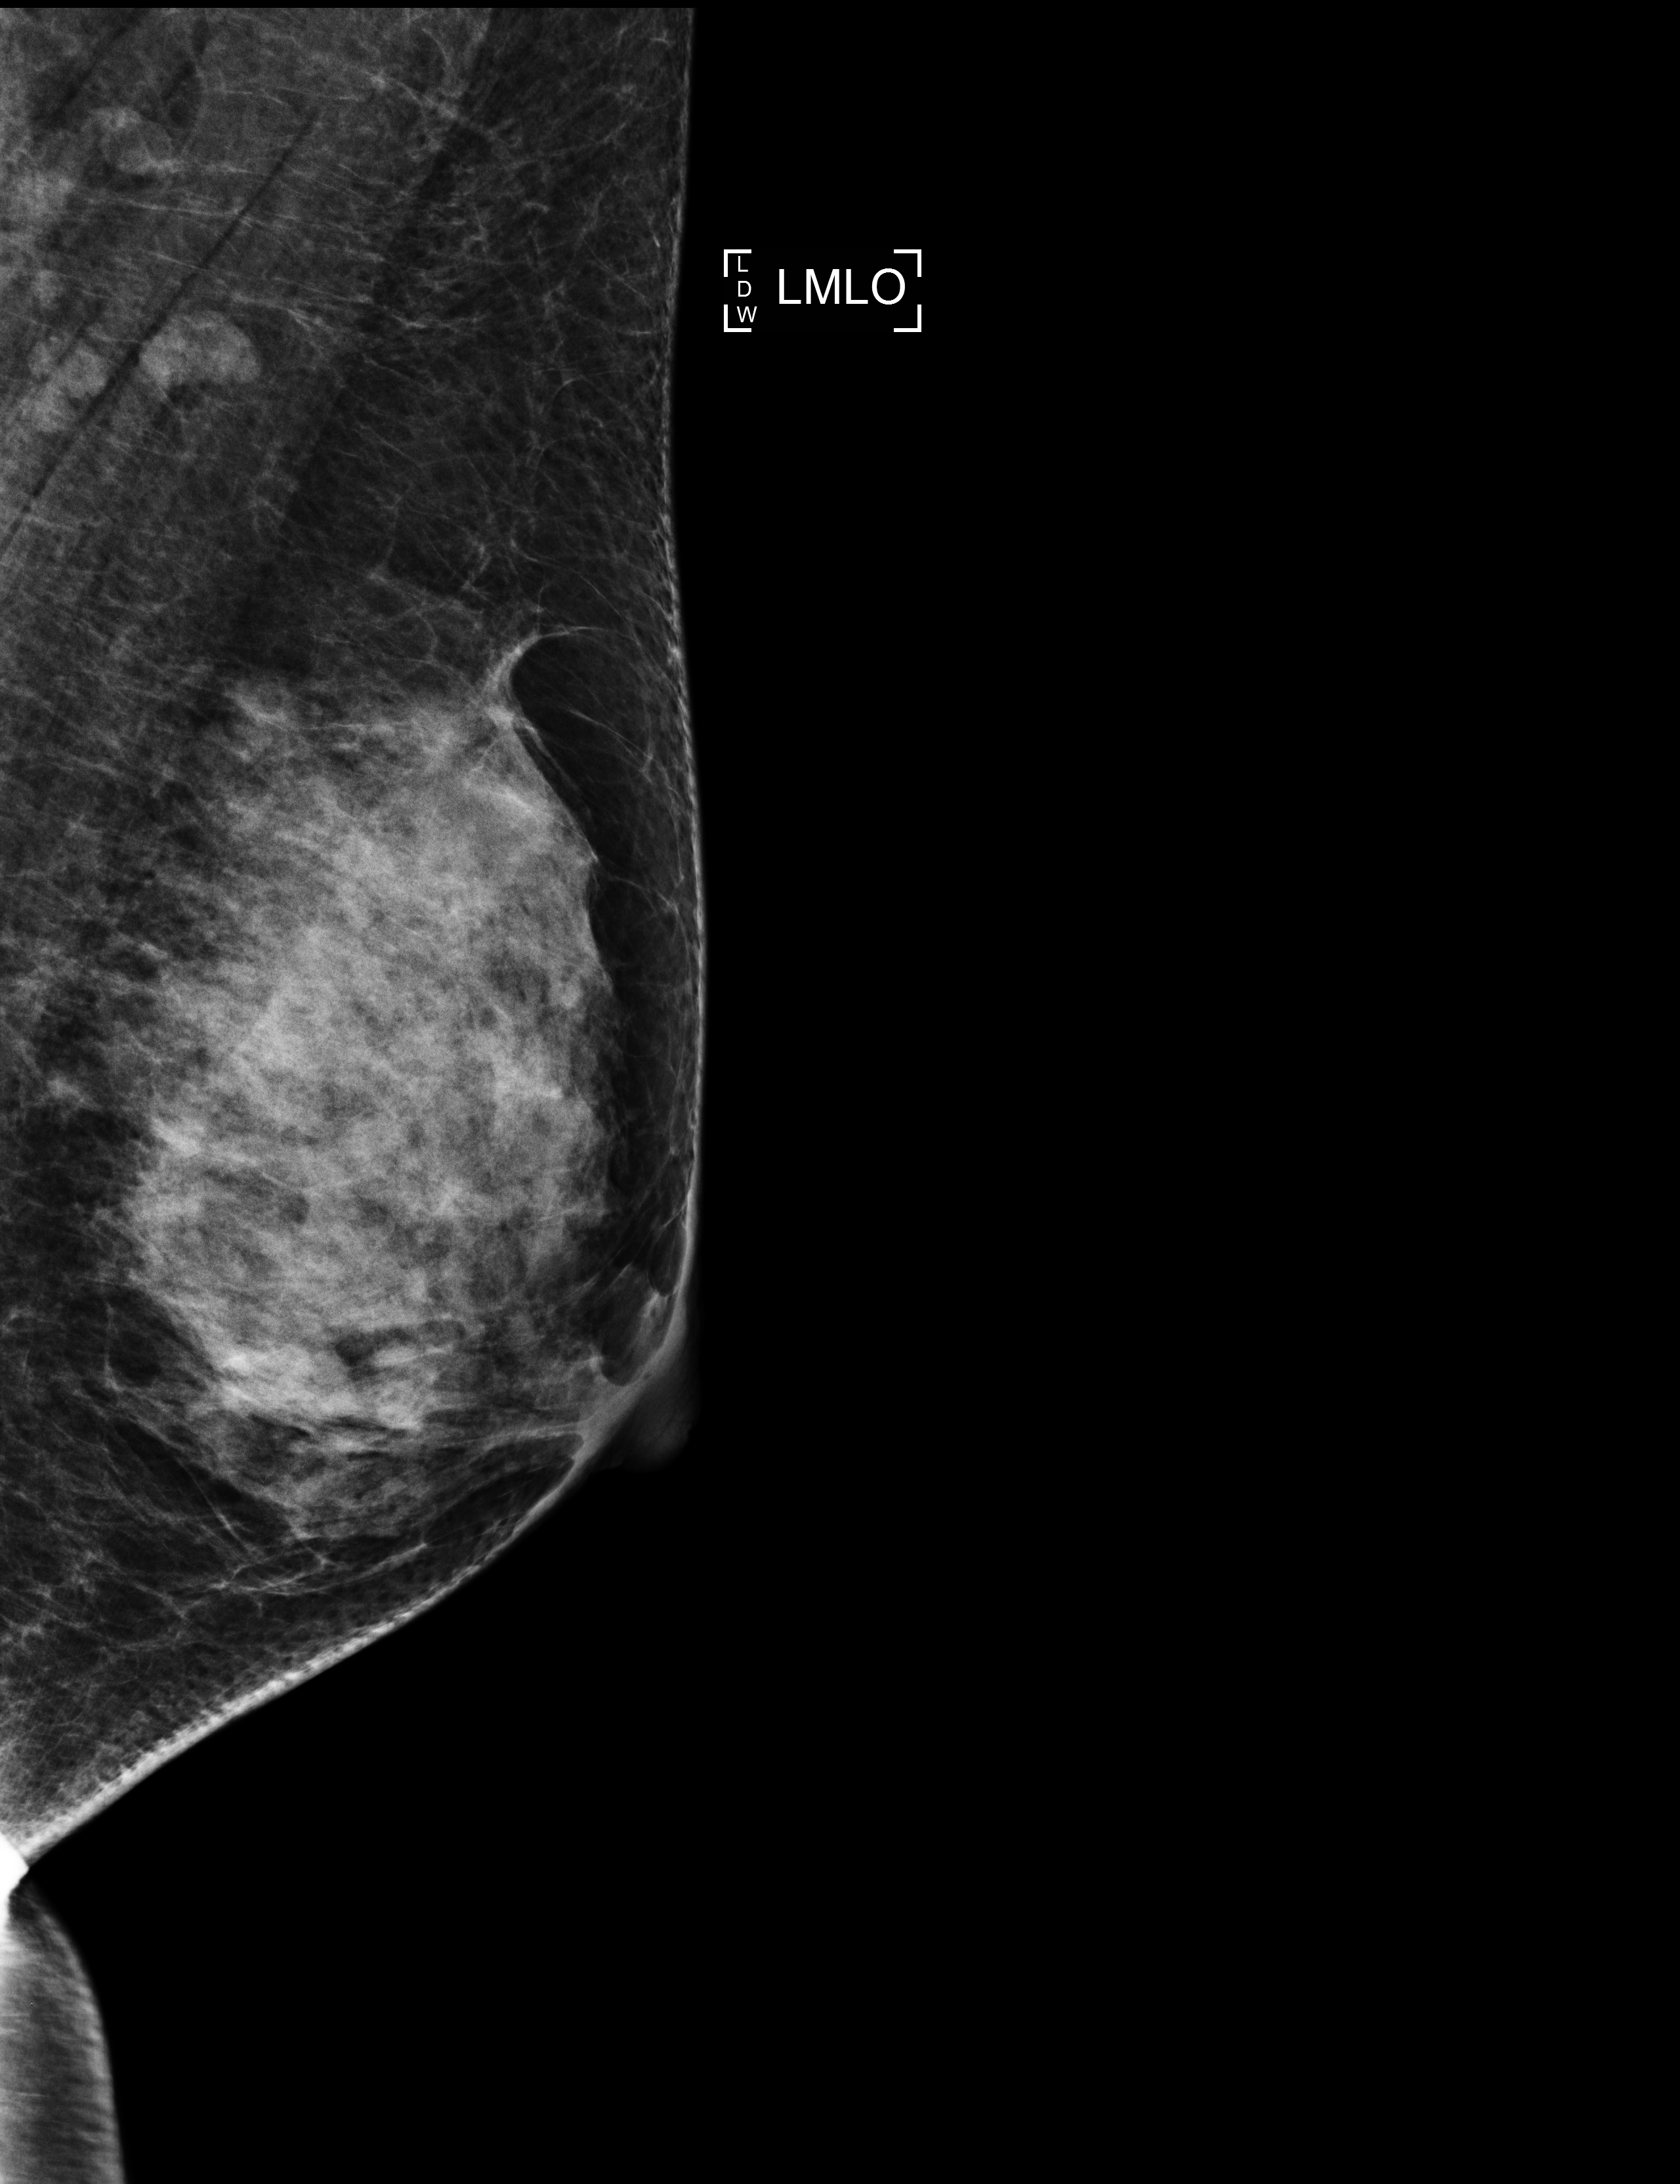
Full-field digital mammogram (FFDM); left breast; MLO view; annual screening mammography examination. Patient: female, 50 years.
Breast density at the screening exam (both breasts): extremely dense (BI-RADS density category d). Final BI-RADS assessment for this screening round (tomosynthesis exam, both breasts): category 1. Recall: no recall after this screen.